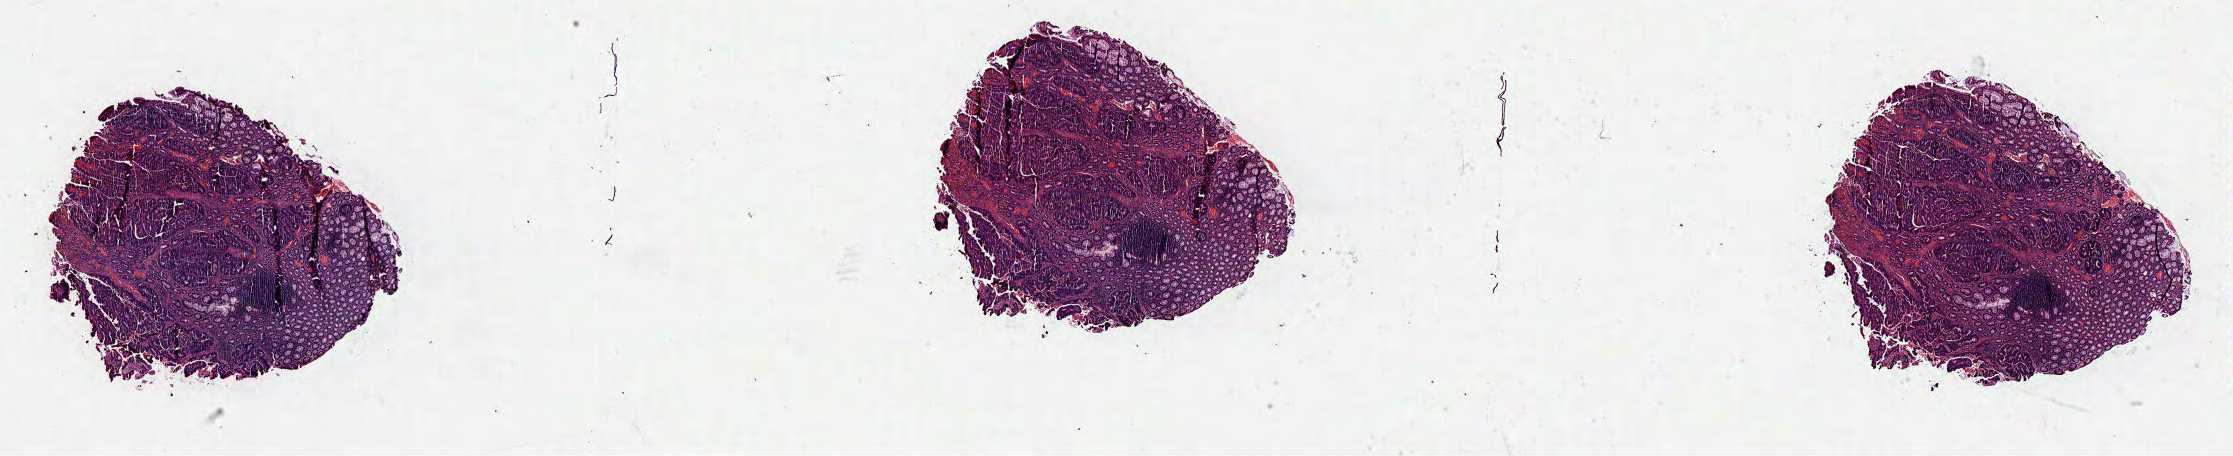
H&E-stained whole-slide image, low-resolution overview of the scanned area, about 36.0 x 7.4 mm (from a 40x scan); formalin-fixed paraffin-embedded (FFPE) diagnostic section; primary tumour sample from the rectum. Female patient; age at initial diagnosis 54 years.
Histologic diagnosis: Adenocarcinoma, NOS.